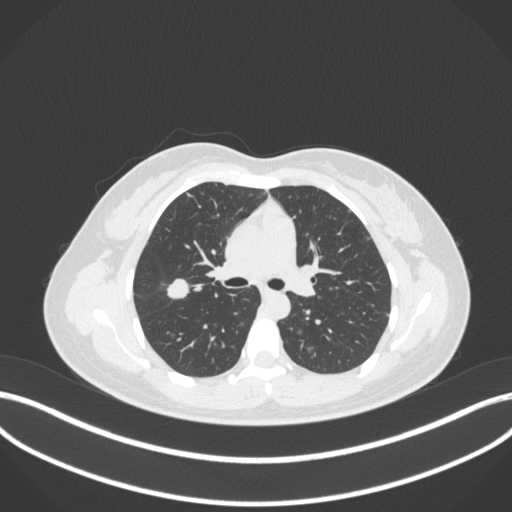
Chest CT, one axial slice. Slice 209 of 214 in the series (ordered by position). Reconstruction kernel B31f. Lung window (W 1500 / L -600 HU). 1 mm slice thickness. 512 × 512 image matrix, field of view 400 × 400 mm. Female patient, age 33 years. Case-level facts recorded for this patient, not image findings: clinical TNM (as recorded): T1c N0 M0; histopathological grade: G2-G3.
Structures marked on this image (rectangle marked by the reading radiologist):
- lung tumour (recorded histology: adenocarcinoma): box from (x=162, y=275) to (x=196, y=310) px